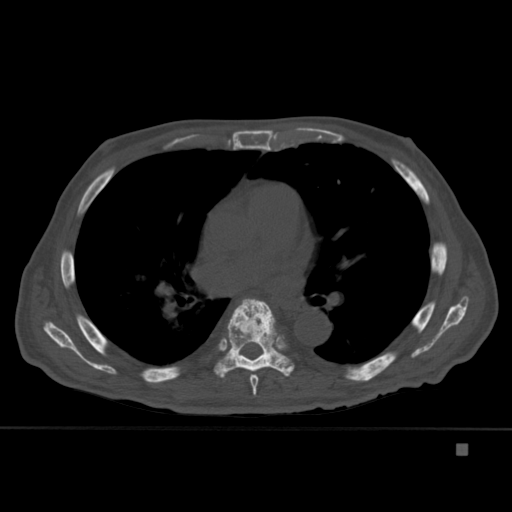
CT including the spine, one axial slice; position 282 of 451 along the scan axis; bone window (W 1800 / L 400 HU); 1.5 mm slice thickness; 512 × 512 image matrix, field of view 378 × 378 mm. Patient: male, 75 years. From the clinical record (not read from this slice): primary cancer: prostate.
Outlined on this slice (semi-automatic segmentation, software-assisted and operator-edited):
- T4 vertebra: box from (x=271, y=323) to (x=278, y=337) px
- T6 vertebra: (x=249, y=374)–(x=259, y=396)
- T7 vertebra: (x=214, y=298)–(x=295, y=378)